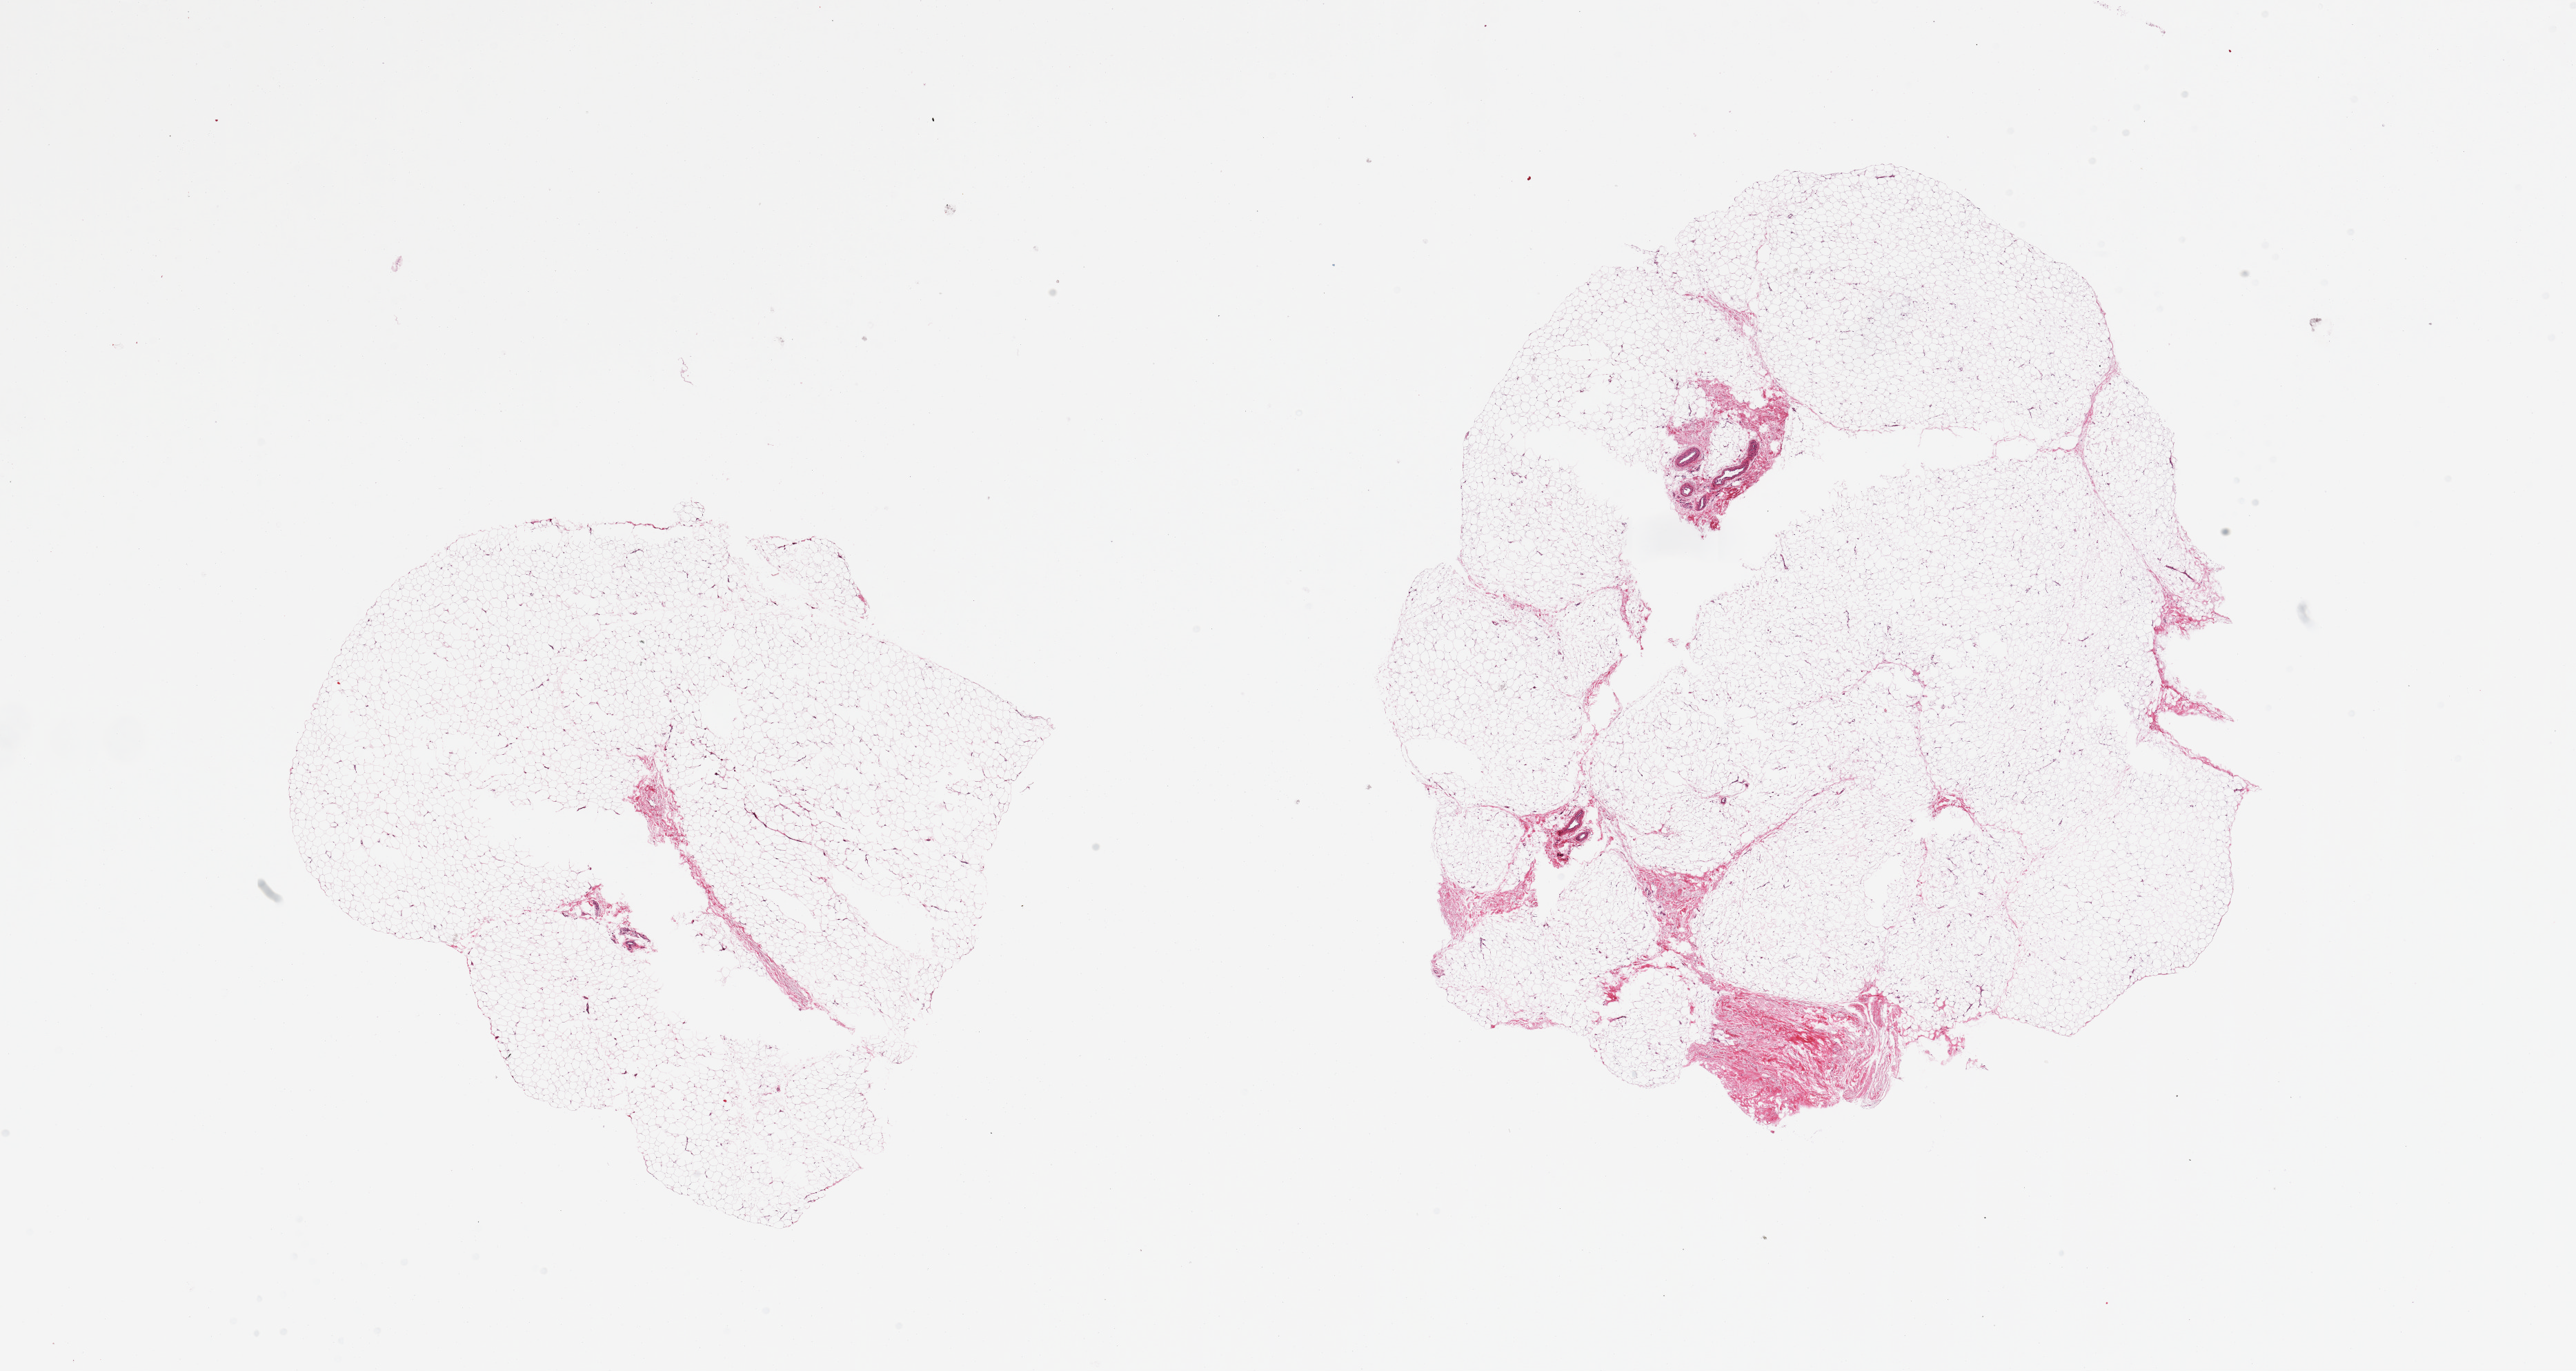
Whole-slide image, hematoxylin and eosin (H&E) stain — whole scanned area (about 29.5 x 15.7 mm) shown as a low-resolution overview. PAXgene-fixed paraffin-embedded (PFPE) section. Target tissue: adipose tissue. Donor tissue sample.
Pathologist's review note for this sample: 2 pieces; predominantly fat with small portion of fibrous and vascular tissue.